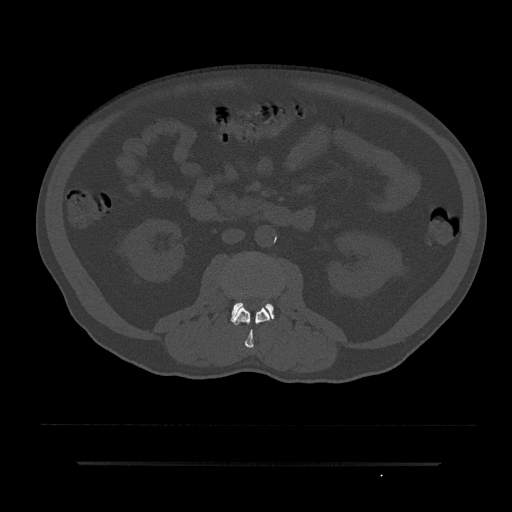
CT including the spine, one axial slice. Position 41 of 797 along the scan axis. Reconstruction kernel Br40s/3. Bone window (W 1800 / L 400 HU). 0.5 mm slice thickness. 512 × 512 image matrix. Male patient, age 59 years. Case-level facts recorded for this patient, not image findings: primary cancer: bile ducts.
Outlined on this slice (semi-automatically segmented with operator editing):
- L2 vertebra: box from (x=233, y=306) to (x=271, y=348) px
- L3 vertebra: (x=231, y=302)–(x=274, y=323)